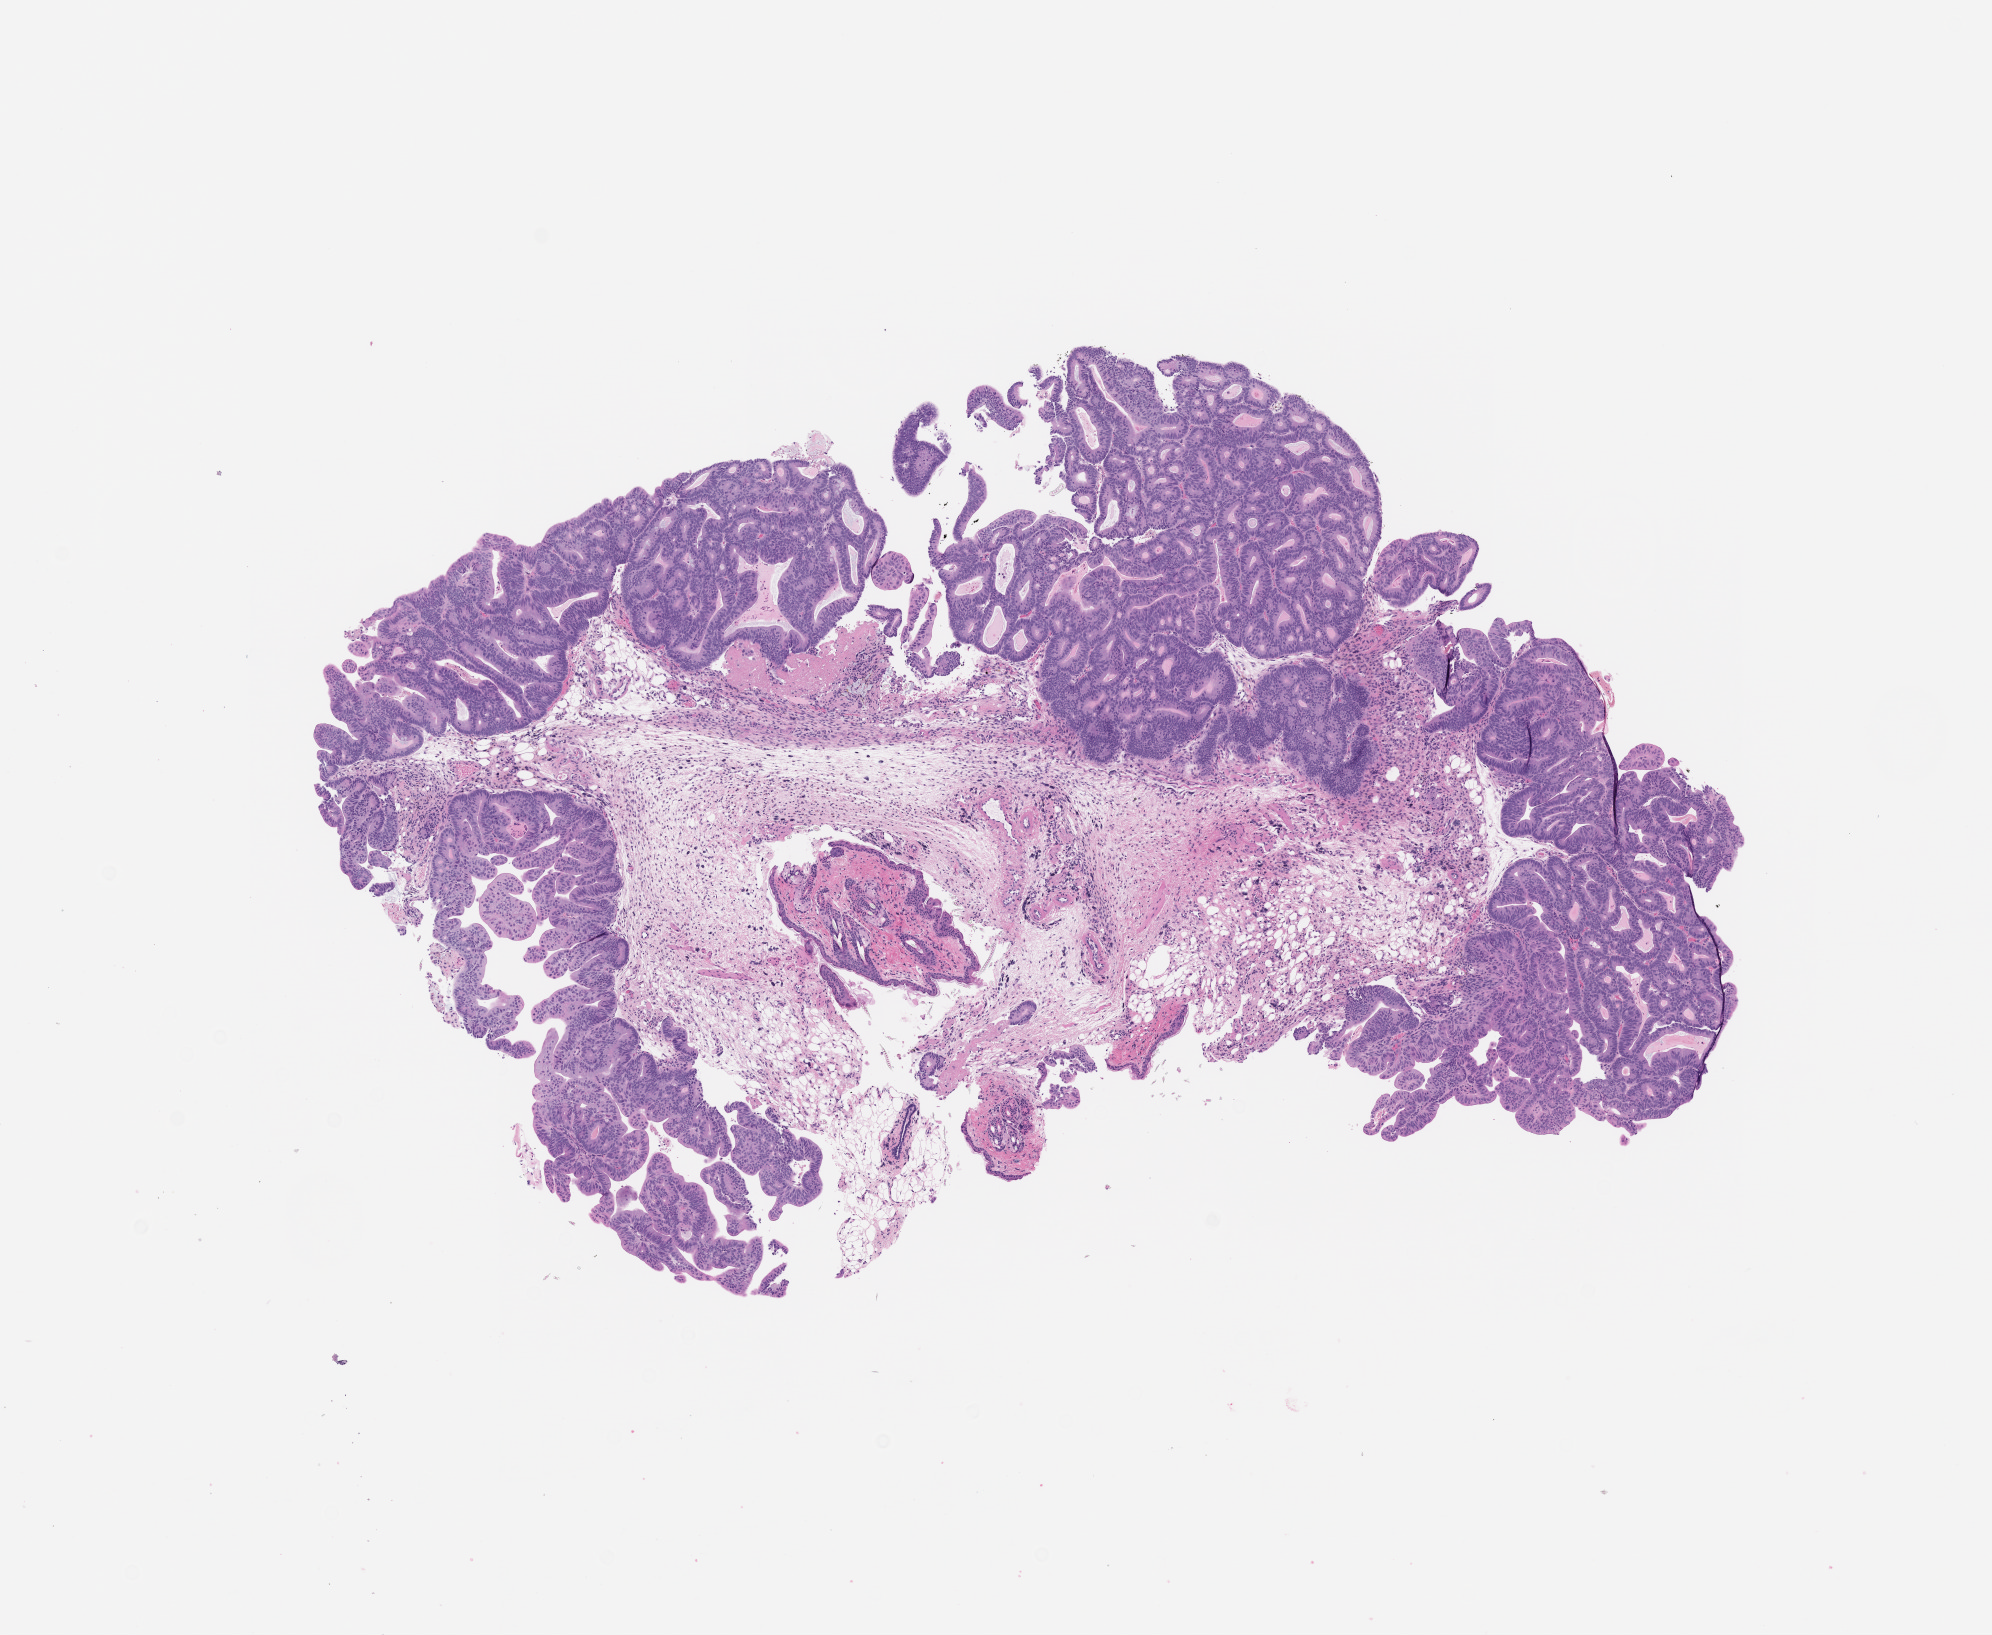
Whole-slide image, hematoxylin and eosin (H&E): patient-derived xenograft (human tumor grown in a mouse), passage 5, shown as a low-resolution overview of the whole scanned area (about 8.0 x 6.6 mm), formalin-fixed paraffin-embedded section, originating tumor site category: colon.
• originating patient diagnosis: Colon Adenocarcinoma